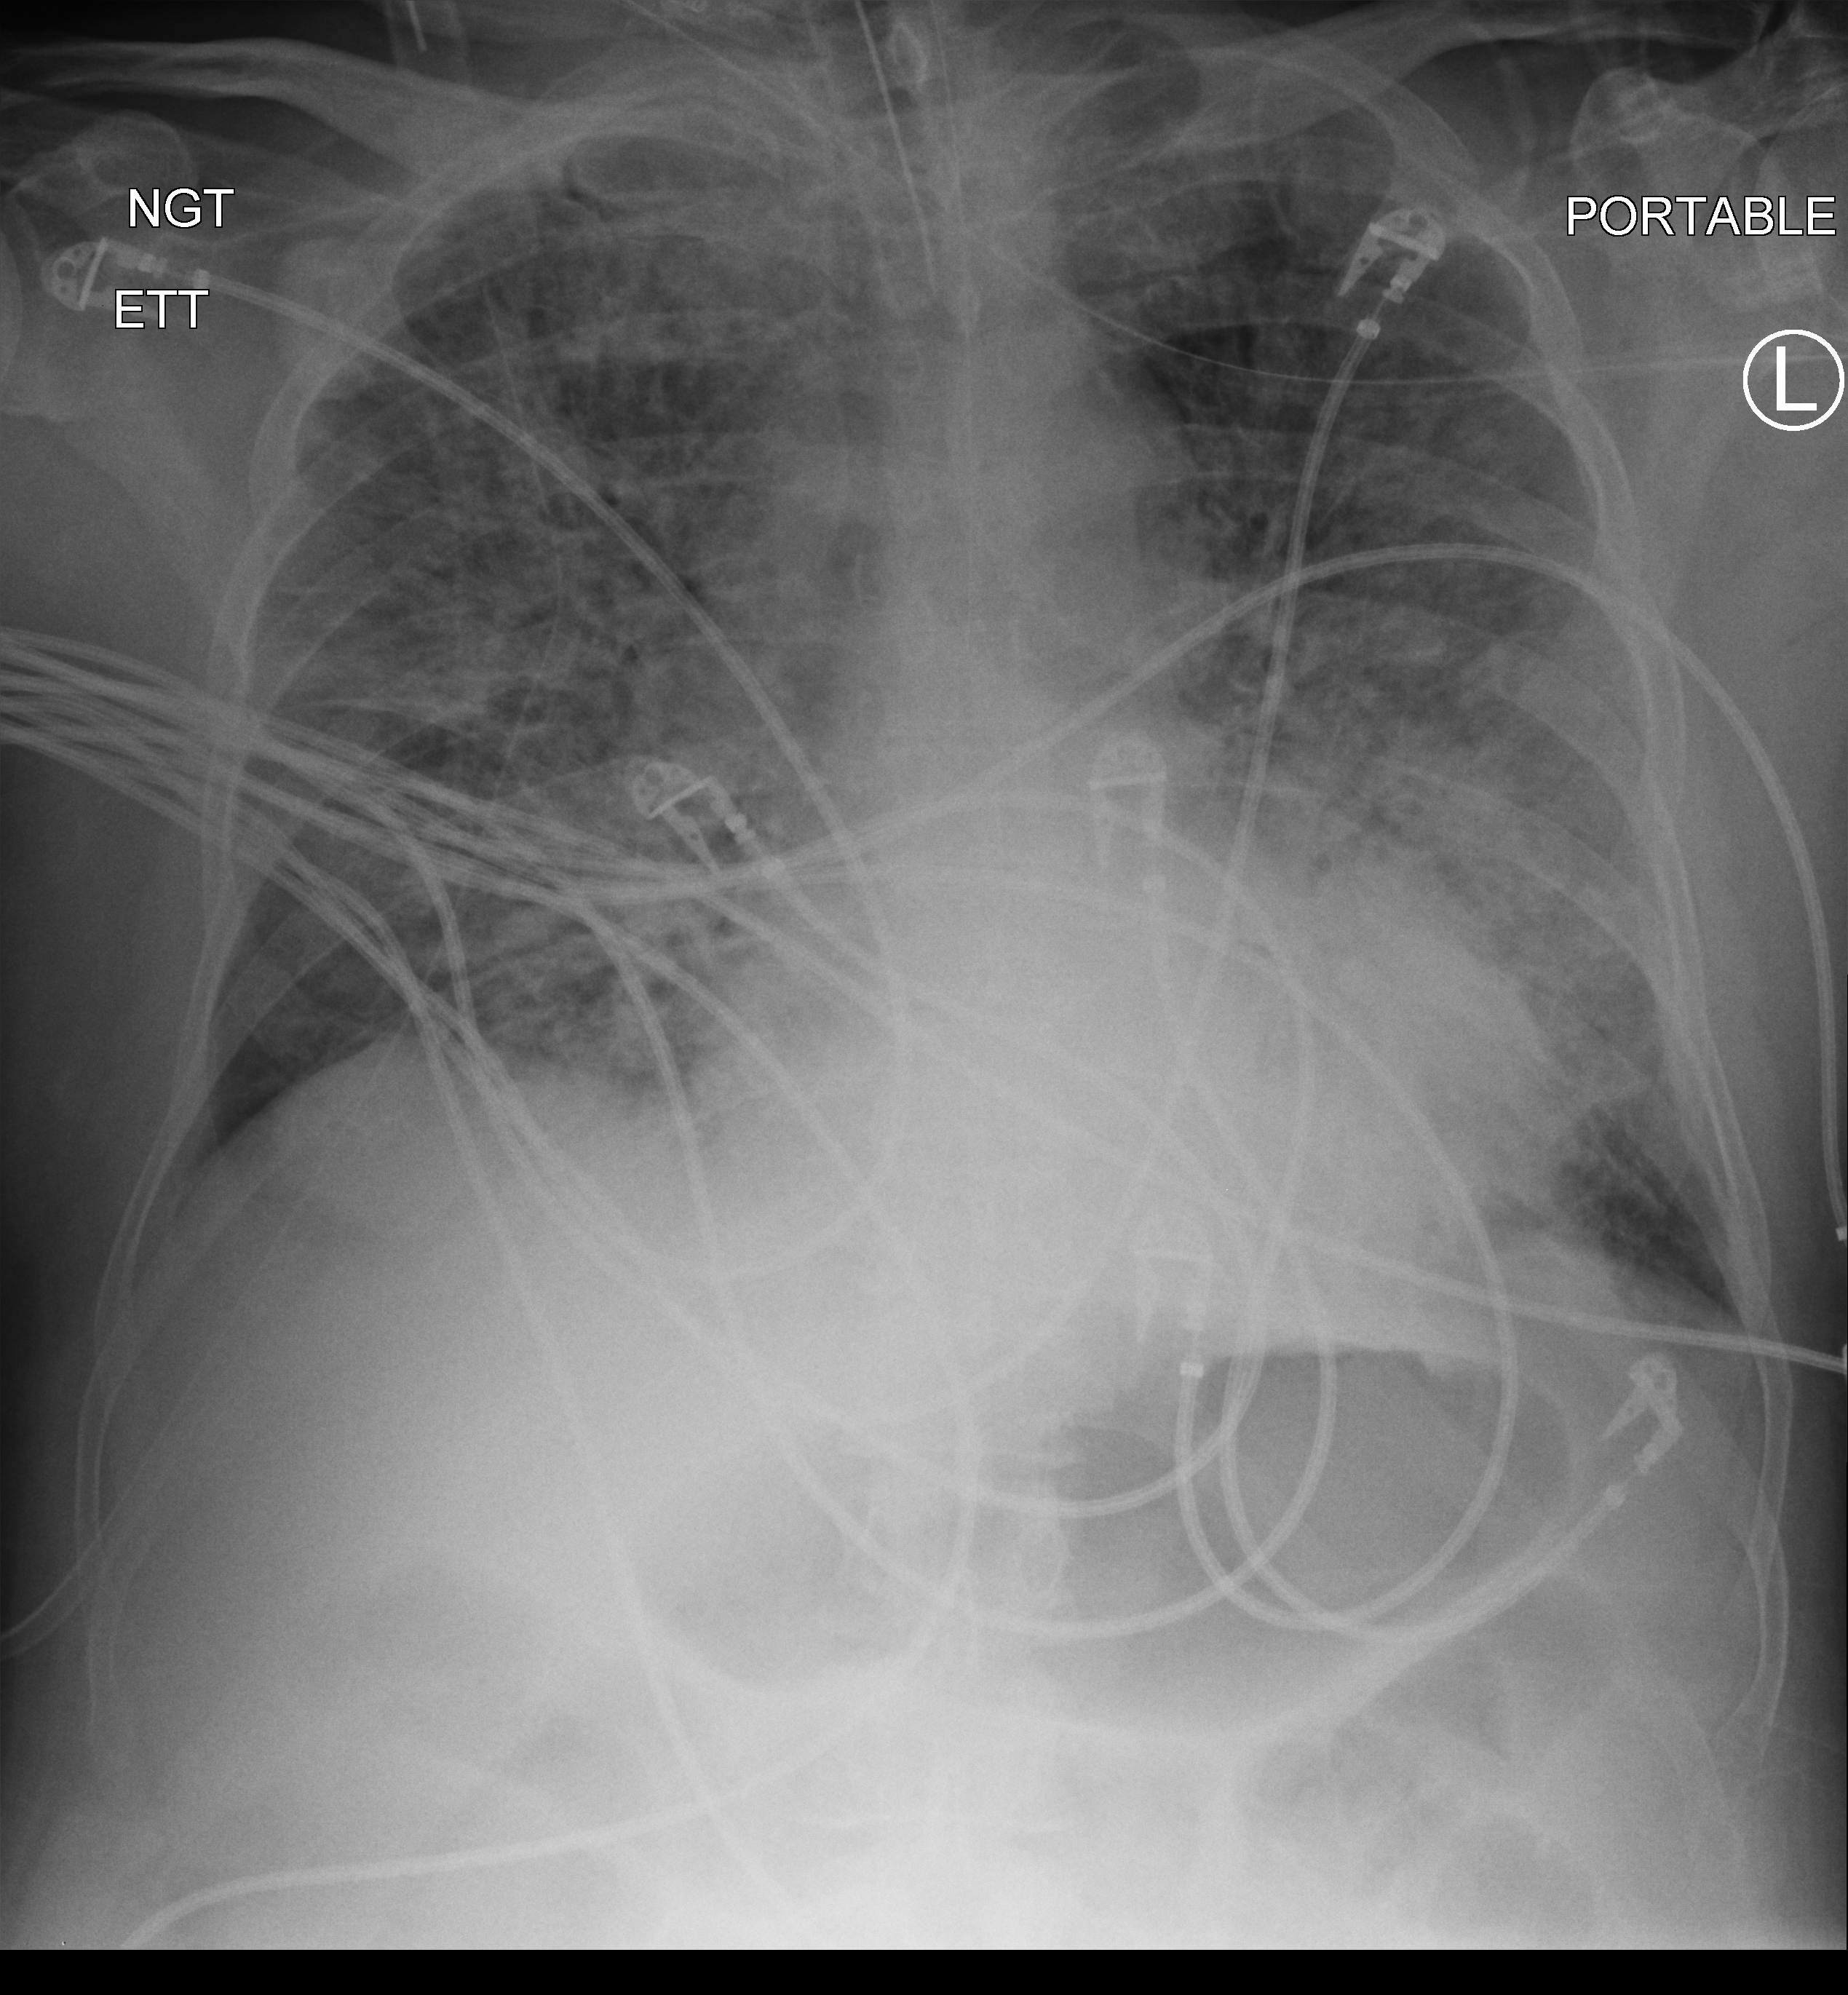
Chest X-ray (portable), anteroposterior (AP) projection. Male patient hospitalised with COVID-19, age 60–74 years.
From the hospital-stay record, not from the radiograph (when in the stay this image was taken is not recorded): mechanically ventilated during this hospital stay: yes; chronic kidney disease (admission record): no; other chronic lung disease (admission record): no.